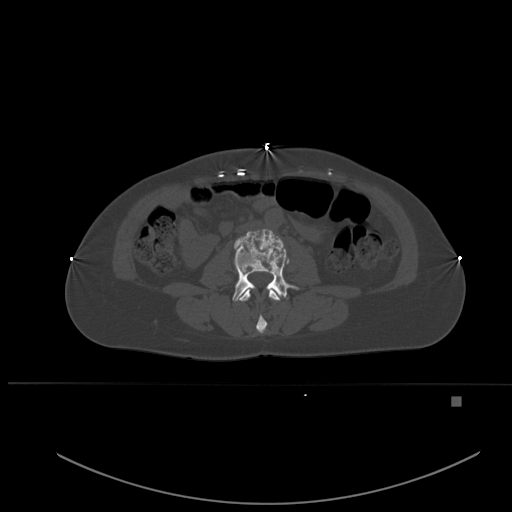
CT including the spine, one axial slice. Slice 198 of 651 in the series (ordered by position). Bone window (W 1800 / L 400 HU). 512 × 512 image matrix. Female patient, age 49 years. Case-level facts recorded for this patient, not image findings: primary cancer: breast.
Annotated regions visible in this slice (semi-automatically segmented with operator editing):
- L2 vertebra: bounding box [x1, y1, x2, y2] px = [238, 289, 281, 333]
- L3 vertebra: [232, 231, 299, 302]